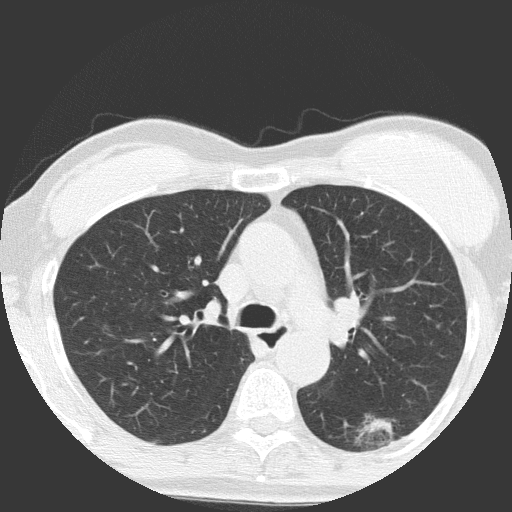
Low-dose screening chest CT, axial slice, baseline annual screen, lung window (W 1500 / L -600 HU), 2 mm slice thickness, lung (sharp) reconstruction kernel (FC51), slice 50 of 149 in the series, 512 × 512 image matrix, field of view 300 × 300 mm. Female, age 64 years at enrolment. Former smoker at enrolment.
Lesion marked by an expert reader, bounding box [x1, y1, x2, y2] px = [332, 398, 420, 468]. Screening reader's record for this exam (one nodule recorded; not confirmed to be the boxed lesion): non-calcified nodule or mass ≥4 mm, right upper lobe, 4 × 4 mm, poorly defined margins, ground glass attenuation. Note: the box lies in the patient's left hemithorax on this image, whereas the reader's record names the right lung; they may be different findings.